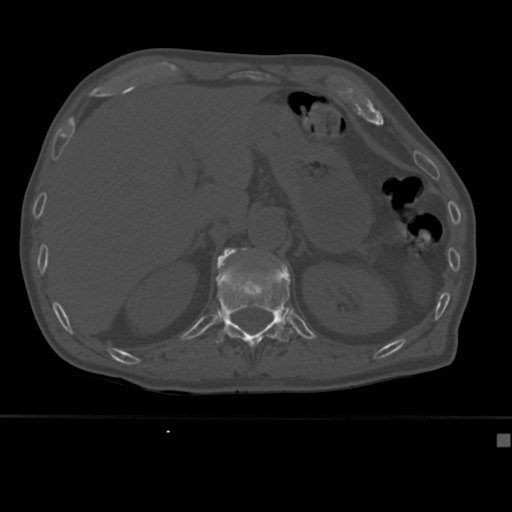
CT including the spine, one axial slice. Slice 189 of 430 in the series (ordered by position). Reconstruction kernel Br40s. 120 kVp. Bone window (W 1800 / L 400 HU). 1.5 mm slice thickness. 512 × 512 image matrix. Male patient, age 64 years. From the clinical record (not read from this slice): primary cancer: uterus.
Outlined on this slice (semi-automatically segmented with operator editing):
- L1 vertebra: bounding box [x1, y1, x2, y2] px = [217, 248, 256, 267]
- T12 vertebra: [215, 257, 293, 347]